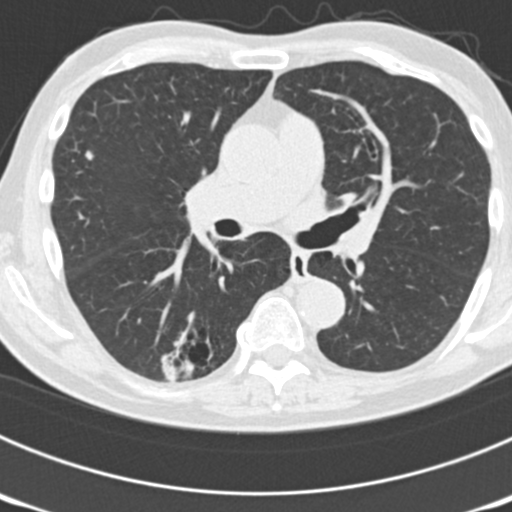
Axial slice from a low-dose chest CT screening exam; third annual screen; lung window (W 1500 / L -600 HU); 2 mm slice thickness; standard (soft-tissue) reconstruction kernel (B30f). Male participant, aged 70 years at enrolment. Current smoker at enrolment.
Expert-annotated lung lesion, bounding box [x1, y1, x2, y2] px = [145, 307, 237, 385]. The screening reader recorded 3 non-calcified nodules or masses ≥4 mm on this exam (right upper lobe, left upper lobe, right lower lobe); which of them this box marks is not recorded. Lung cancer was diagnosed 14 days after this screen: bronchiolo-alveolar adenocarcinoma, NOS, right lower lobe, poorly differentiated (G3), stage IB (AJCC 6th edition), 30 mm at pathology.